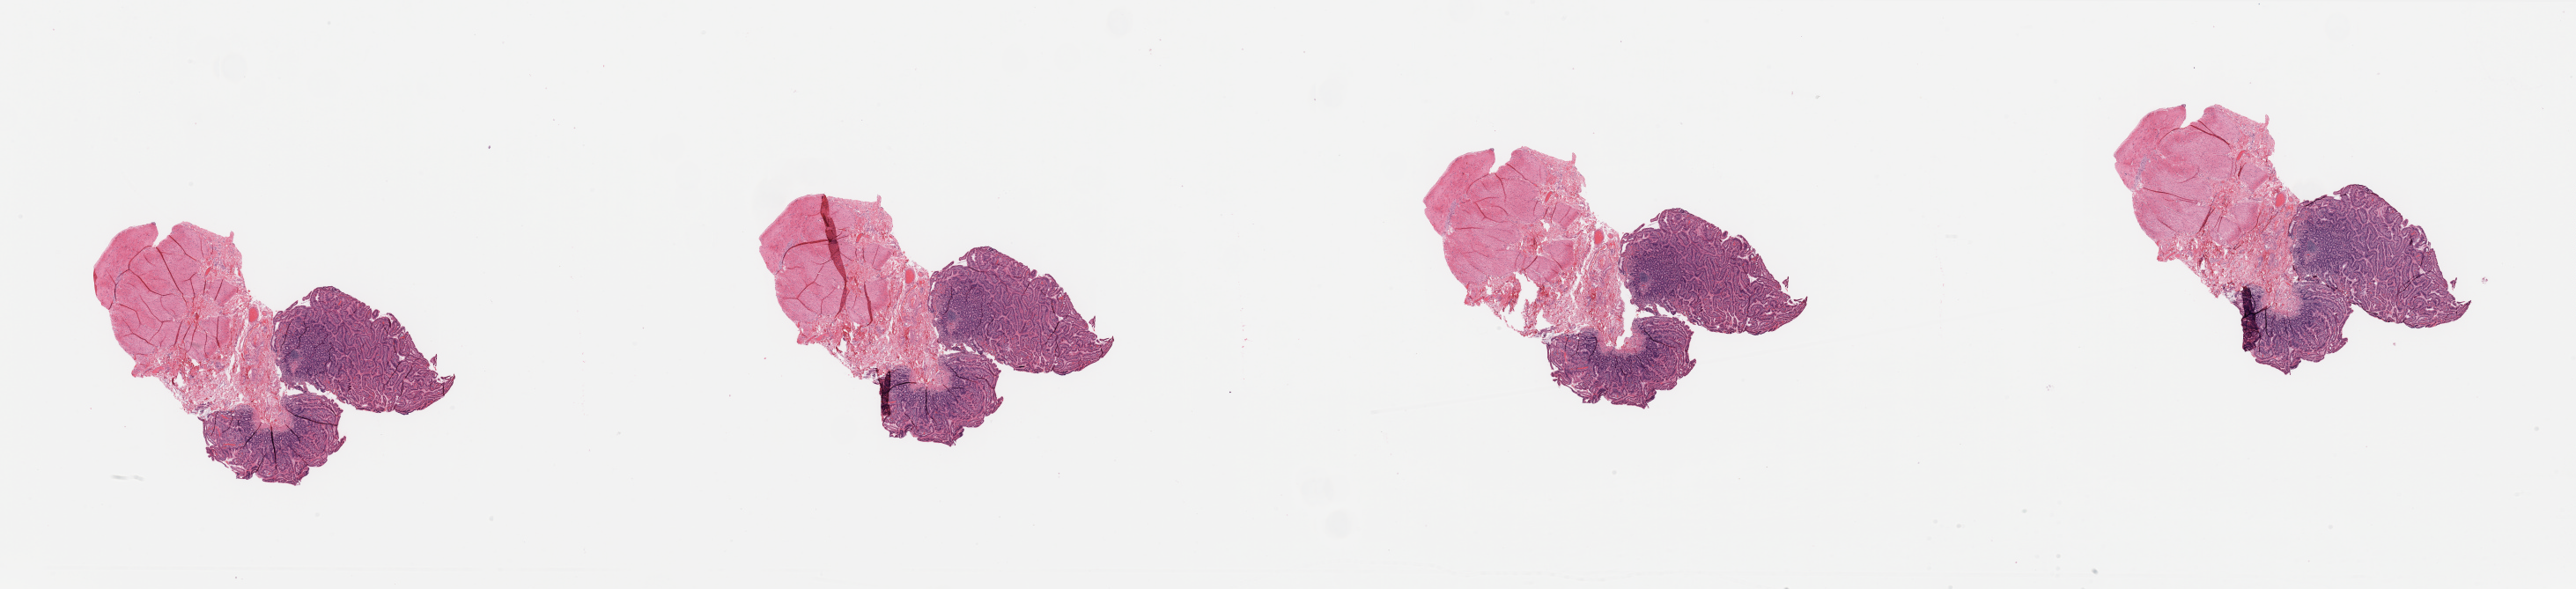
Hematoxylin and eosin (H&E) stained whole-slide image, shown as a low-resolution overview of the whole scanned area (about 46.3 x 10.6 mm, acquisition: 20x scan); normal (non-tumour) tissue sample, pancreas. Patient: male, age 65 years.
• this section: normal (non-tumour) tissue from the same patient
• patient diagnosis: Infiltrating duct carcinoma, NOS